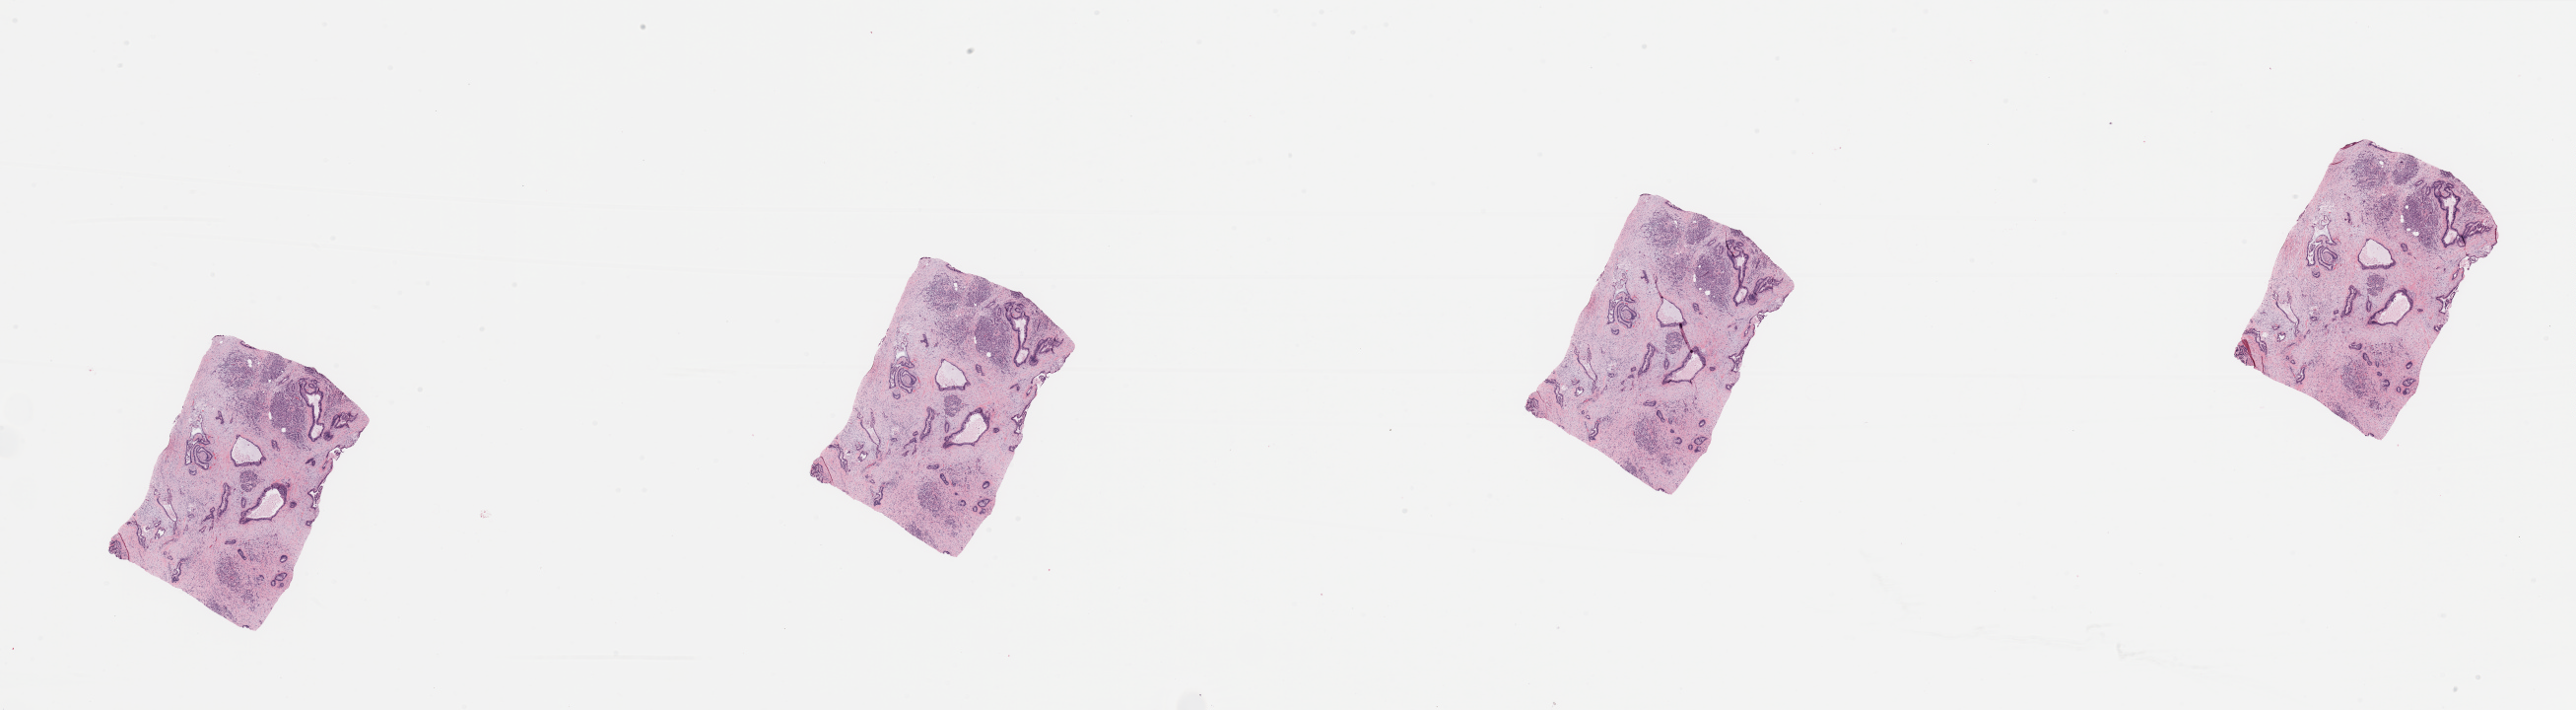
Whole-slide histology image, H&E-stained — a low-resolution overview of the entire scanned area, about 41.3 x 11.4 mm (slide scanned at 20x), tumour tissue sample, sampled site: pancreas. Female, 78 y/o. Histologic grade: G2 (moderately differentiated). Pathologist review of this section (percent, as recorded): tumour nuclei 15%, necrosis 0%.
Diagnosis: Infiltrating duct carcinoma, NOS. AJCC pathologic stage: IIB. Primary tumour site (as recorded): head.